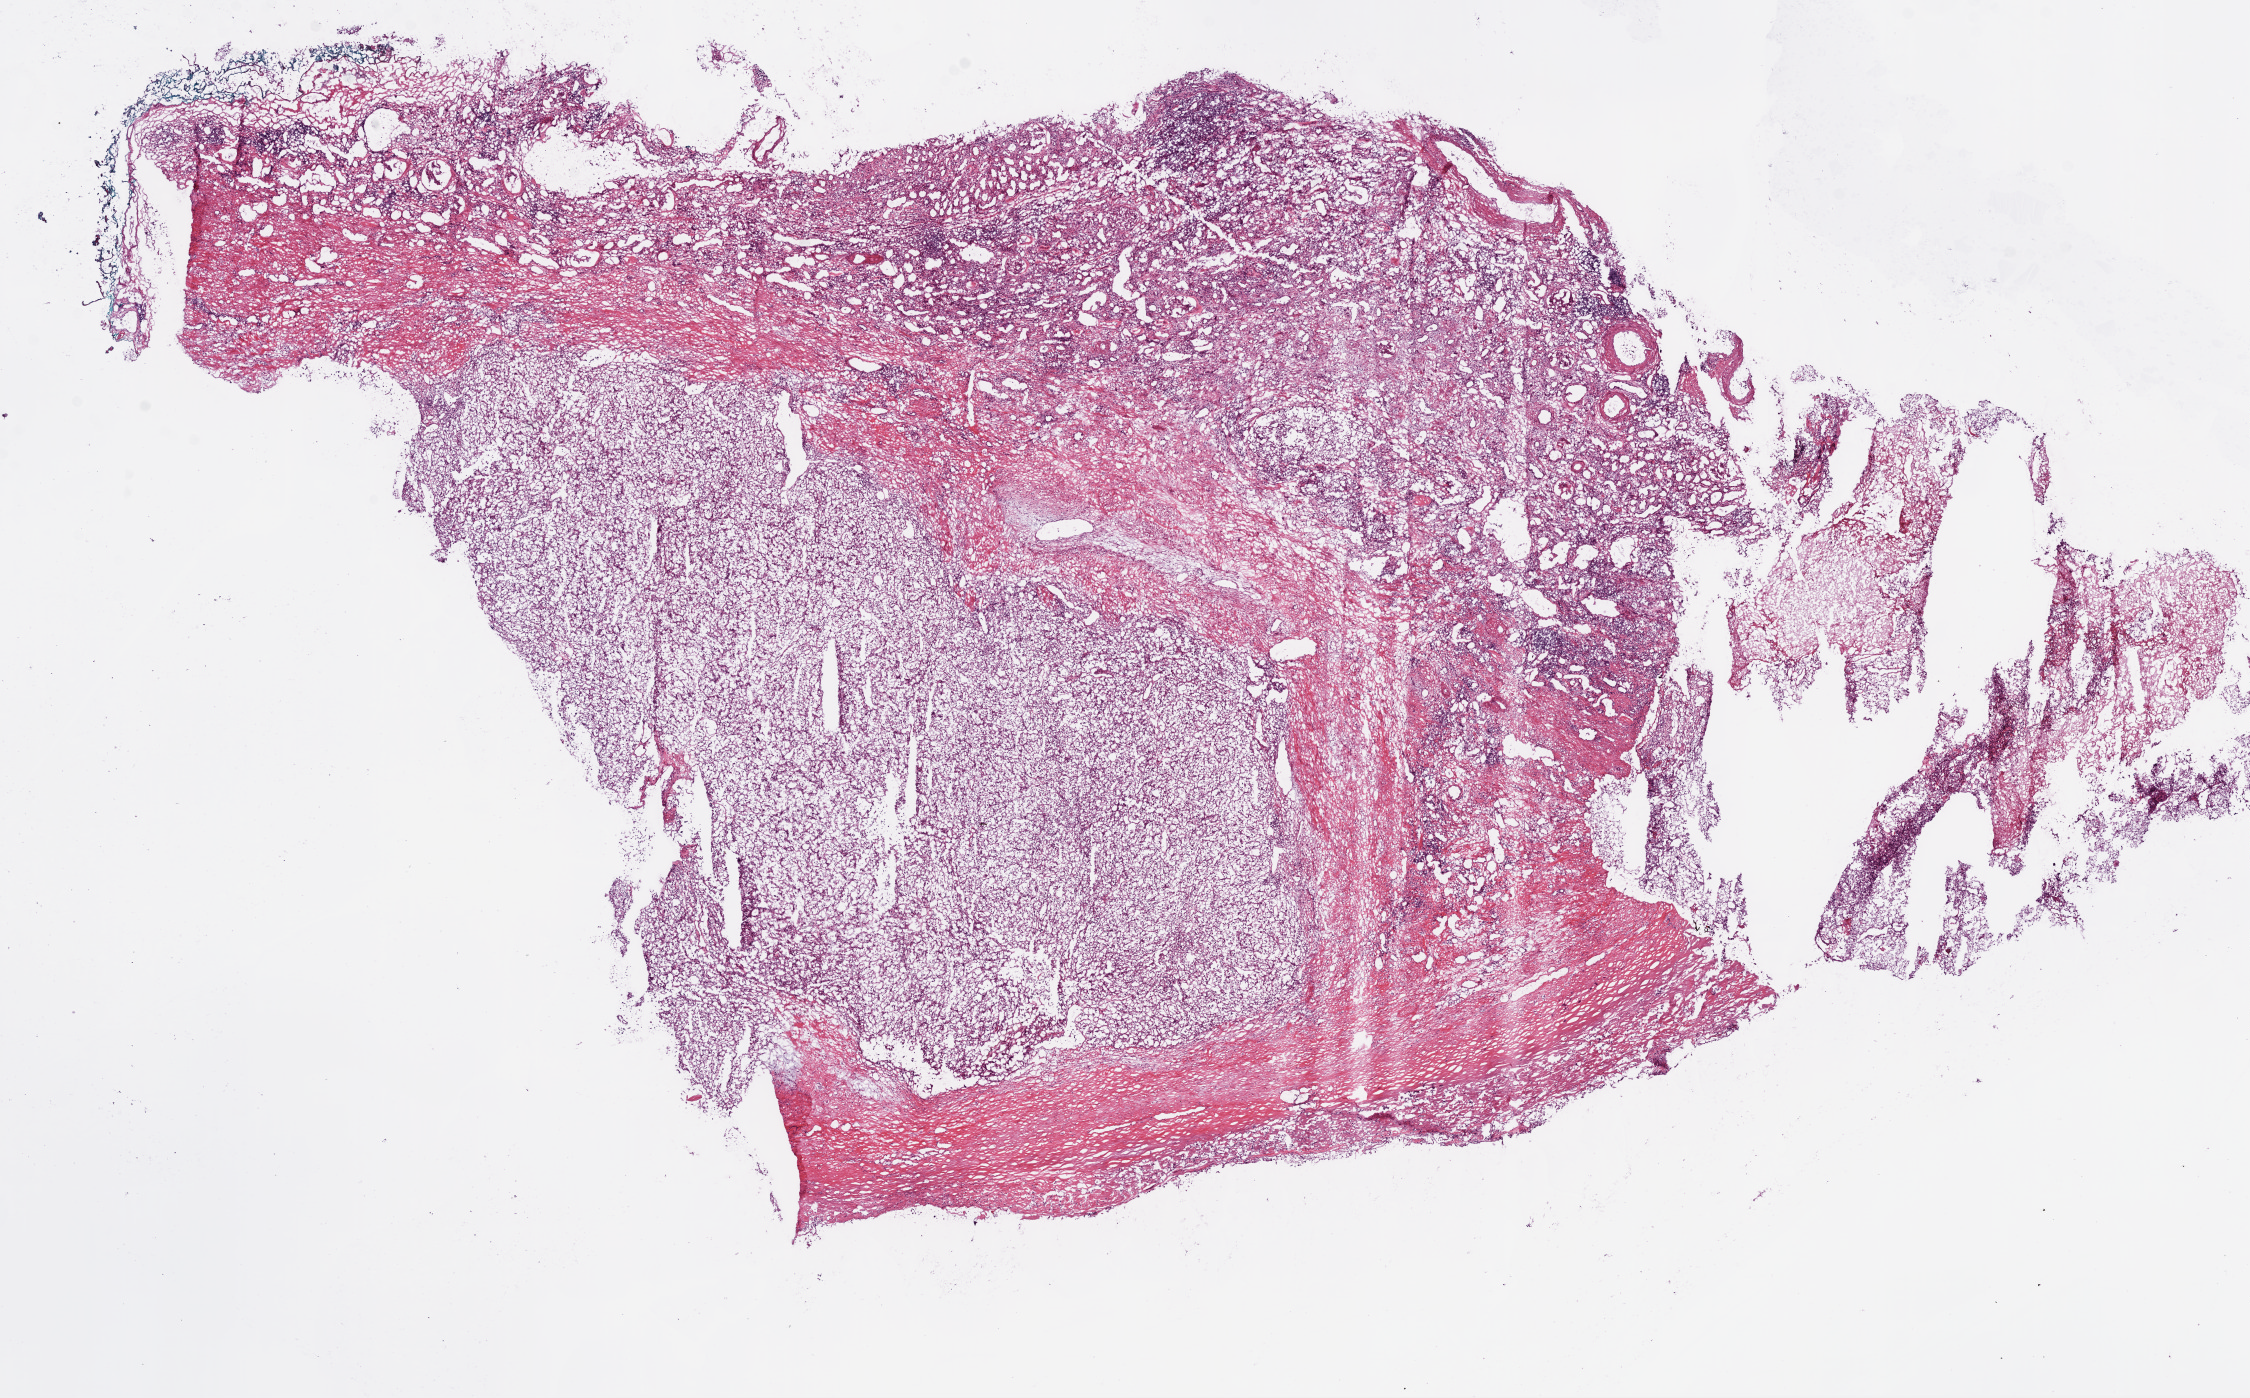
Digitized H&E-stained tissue section (whole slide) — shown as a low-resolution overview of the whole scanned area (about 18.1 x 11.2 mm). Frozen section. Primary tumour sample from the kidney. Male, age 59 years at initial diagnosis. Histologic grade: G2 (moderately differentiated). Slide review estimates, as recorded: tumour cells 80%, tumour nuclei 90%, normal cells 0%, stromal cells 0%, necrosis 20%.
• AJCC pathologic stage: I
• TNM: T1b NX M0
• histologic diagnosis: Clear cell adenocarcinoma, NOS